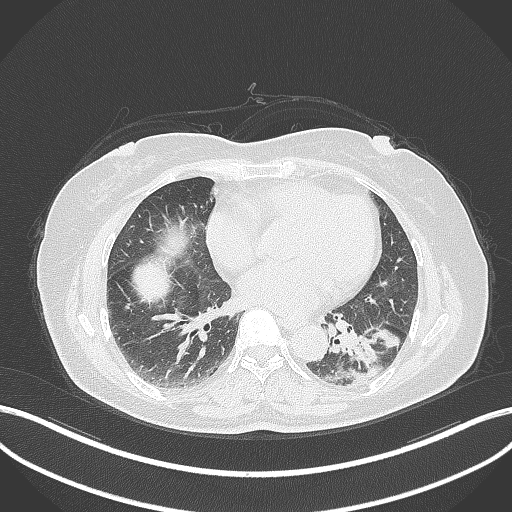
Chest CT, one axial slice. Position 157 of 311 along the scan axis. 120 kVp. Lung window (W 1500 / L -600 HU). 1 mm slice thickness. 512 × 512 image matrix. Female patient, age 59 years. Case-level facts recorded for this patient, not image findings: clinical TNM (as recorded): T2a N0 M0; histopathological grade: G2-3.
Structures marked on this image (bounding box drawn by a radiologist):
- lung tumour (recorded histology: adenocarcinoma): bounding box [x1, y1, x2, y2] px = [344, 325, 404, 374]